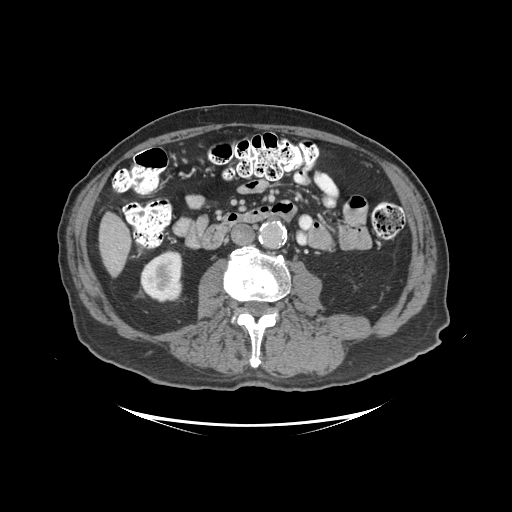
Contrast-enhanced abdominal CT (liver protocol), one axial slice; slice 27 of 99 in the series (ordered by position); reconstruction kernel STANDARD; 140 kVp; soft-tissue window (W 400 / L 40 HU); 512 × 512 image matrix. From the clinical record (not read from this slice): diagnosis: hepatocellular carcinoma (patient treated with transarterial chemoembolisation; whether this scan precedes or follows treatment is not stated here); TNM stage (as recorded): Stage-I.
Outlined on this slice (semi-automatically segmented with operator editing):
- liver parenchyma outside the tumour (the mass and vessels are separate outlines, so this box may not span the whole liver): bounding box [x1, y1, x2, y2] px = [98, 212, 130, 276]